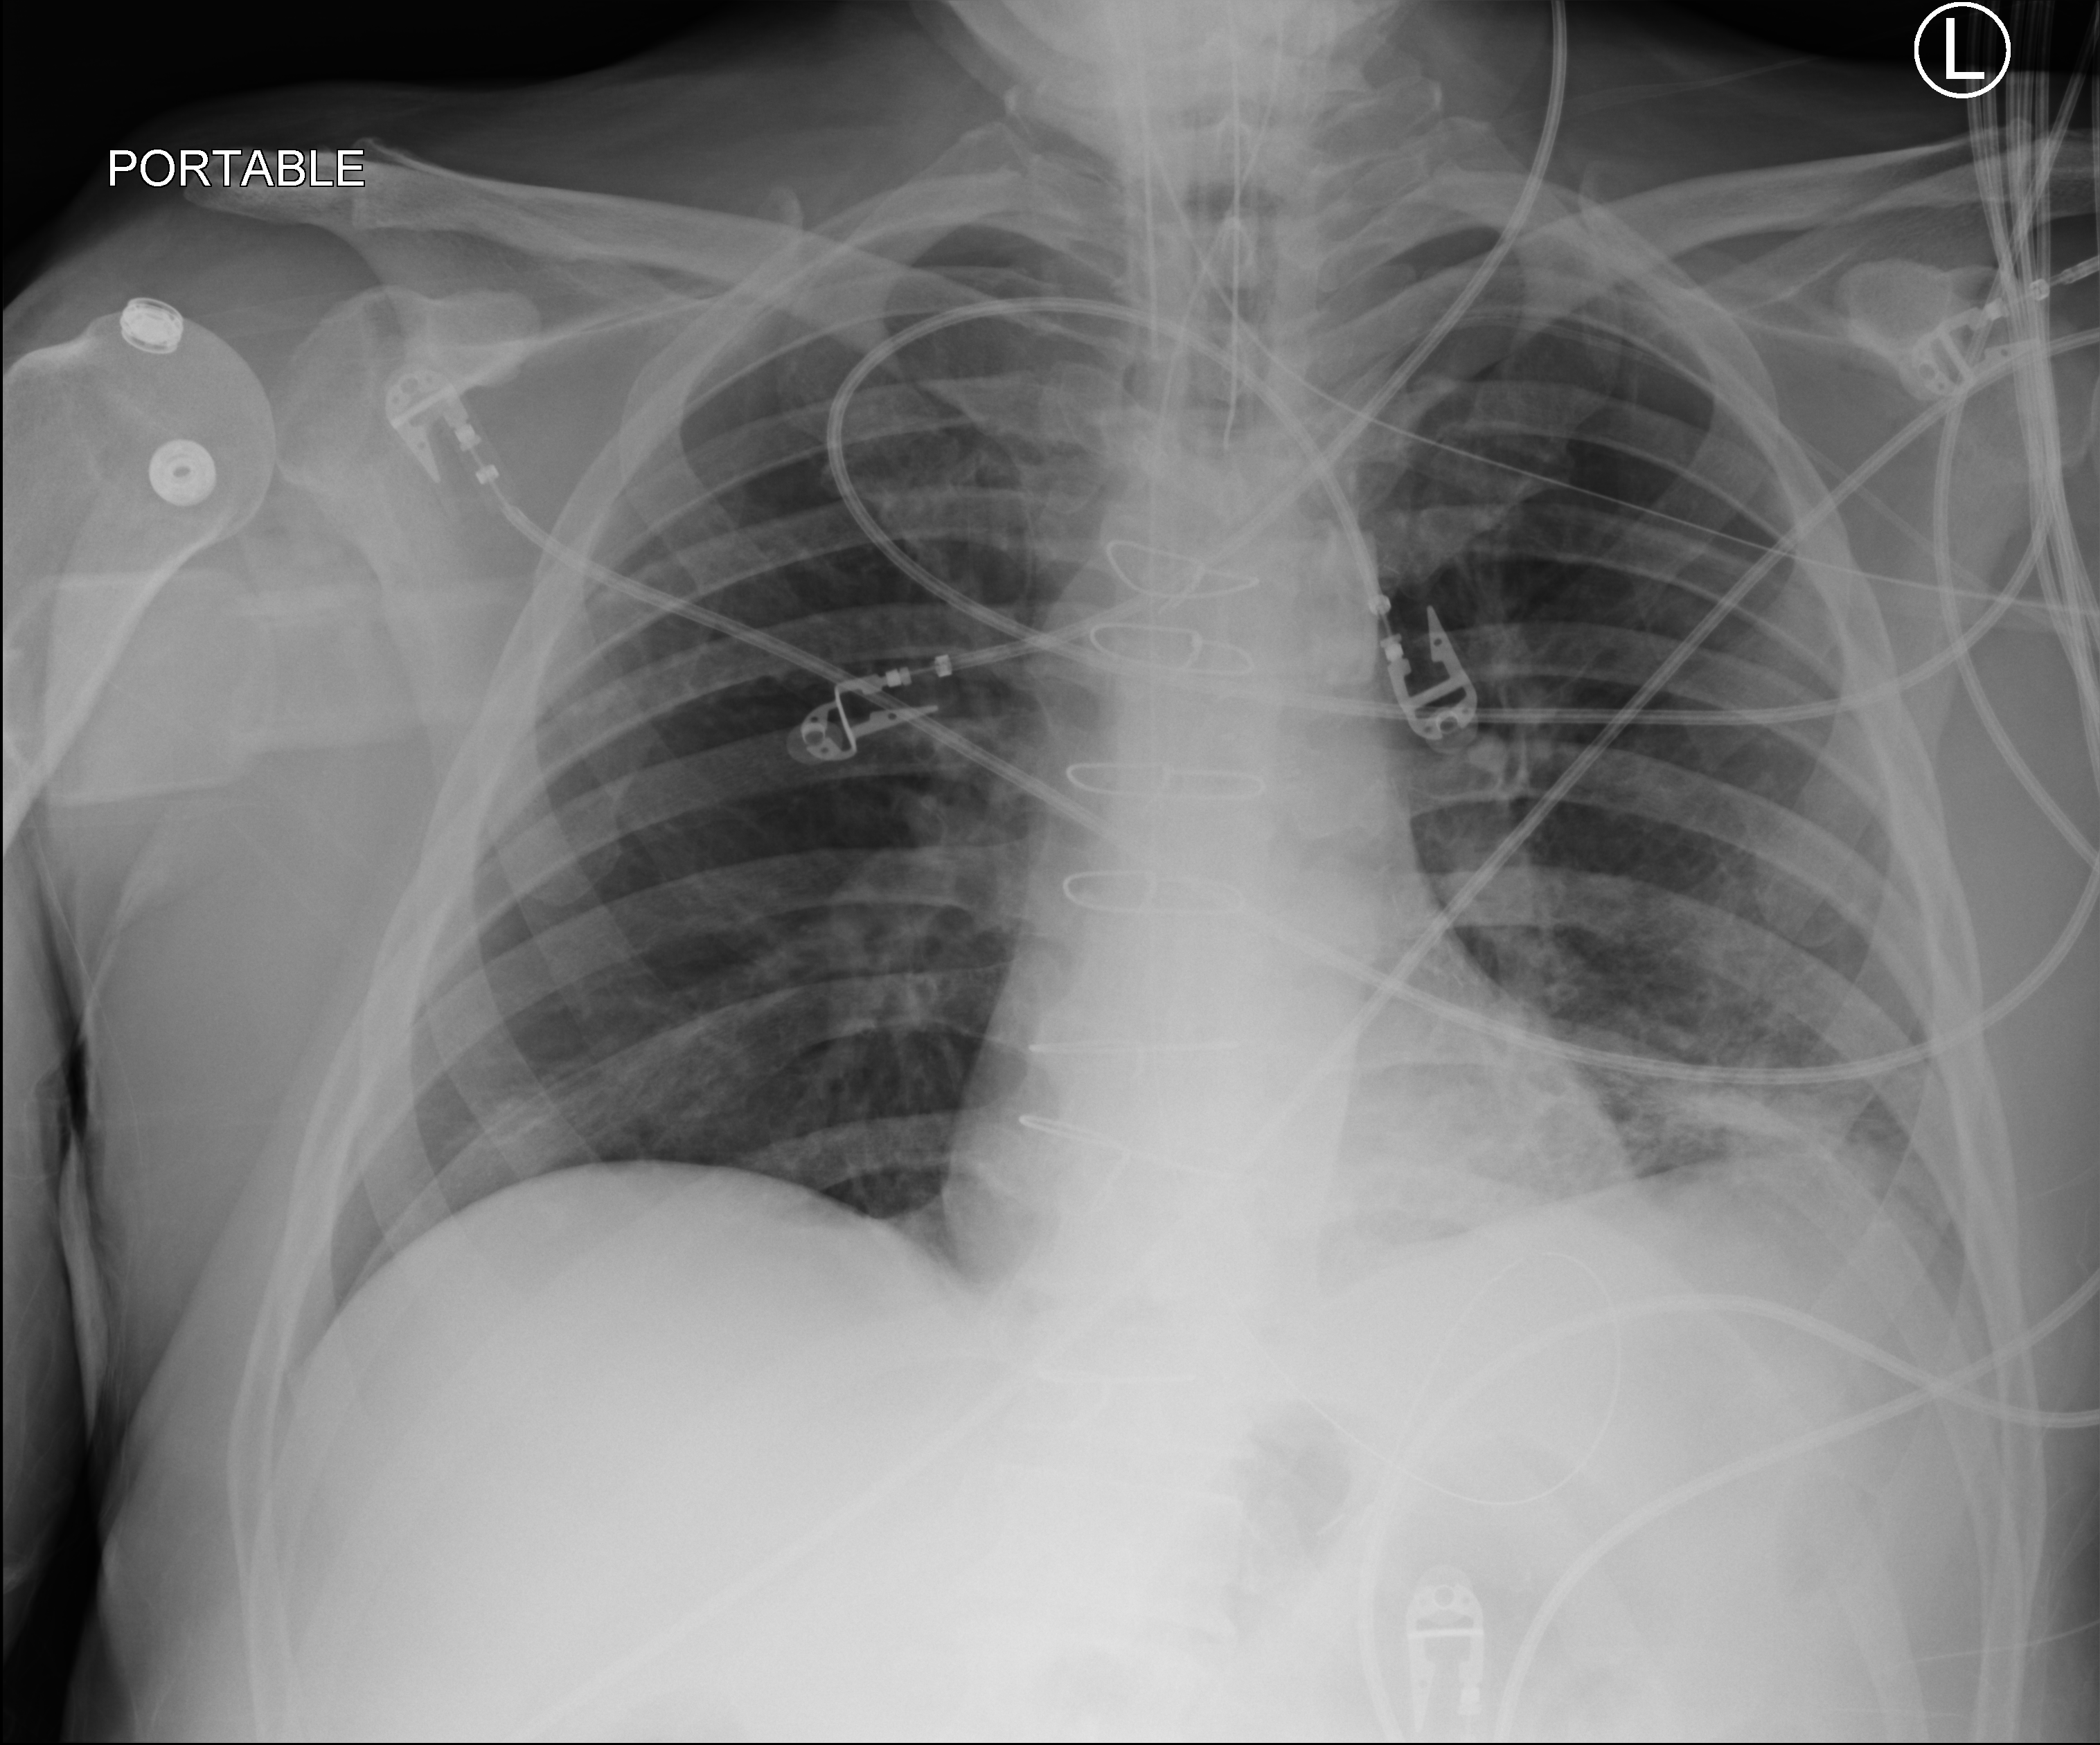
Portable chest radiograph, anteroposterior (AP) projection. Patient hospitalised with COVID-19; male, aged 60–74 years.
From the hospital-stay record, not from the radiograph (when in the stay this image was taken is not recorded):
- other chronic lung disease (admission record): no